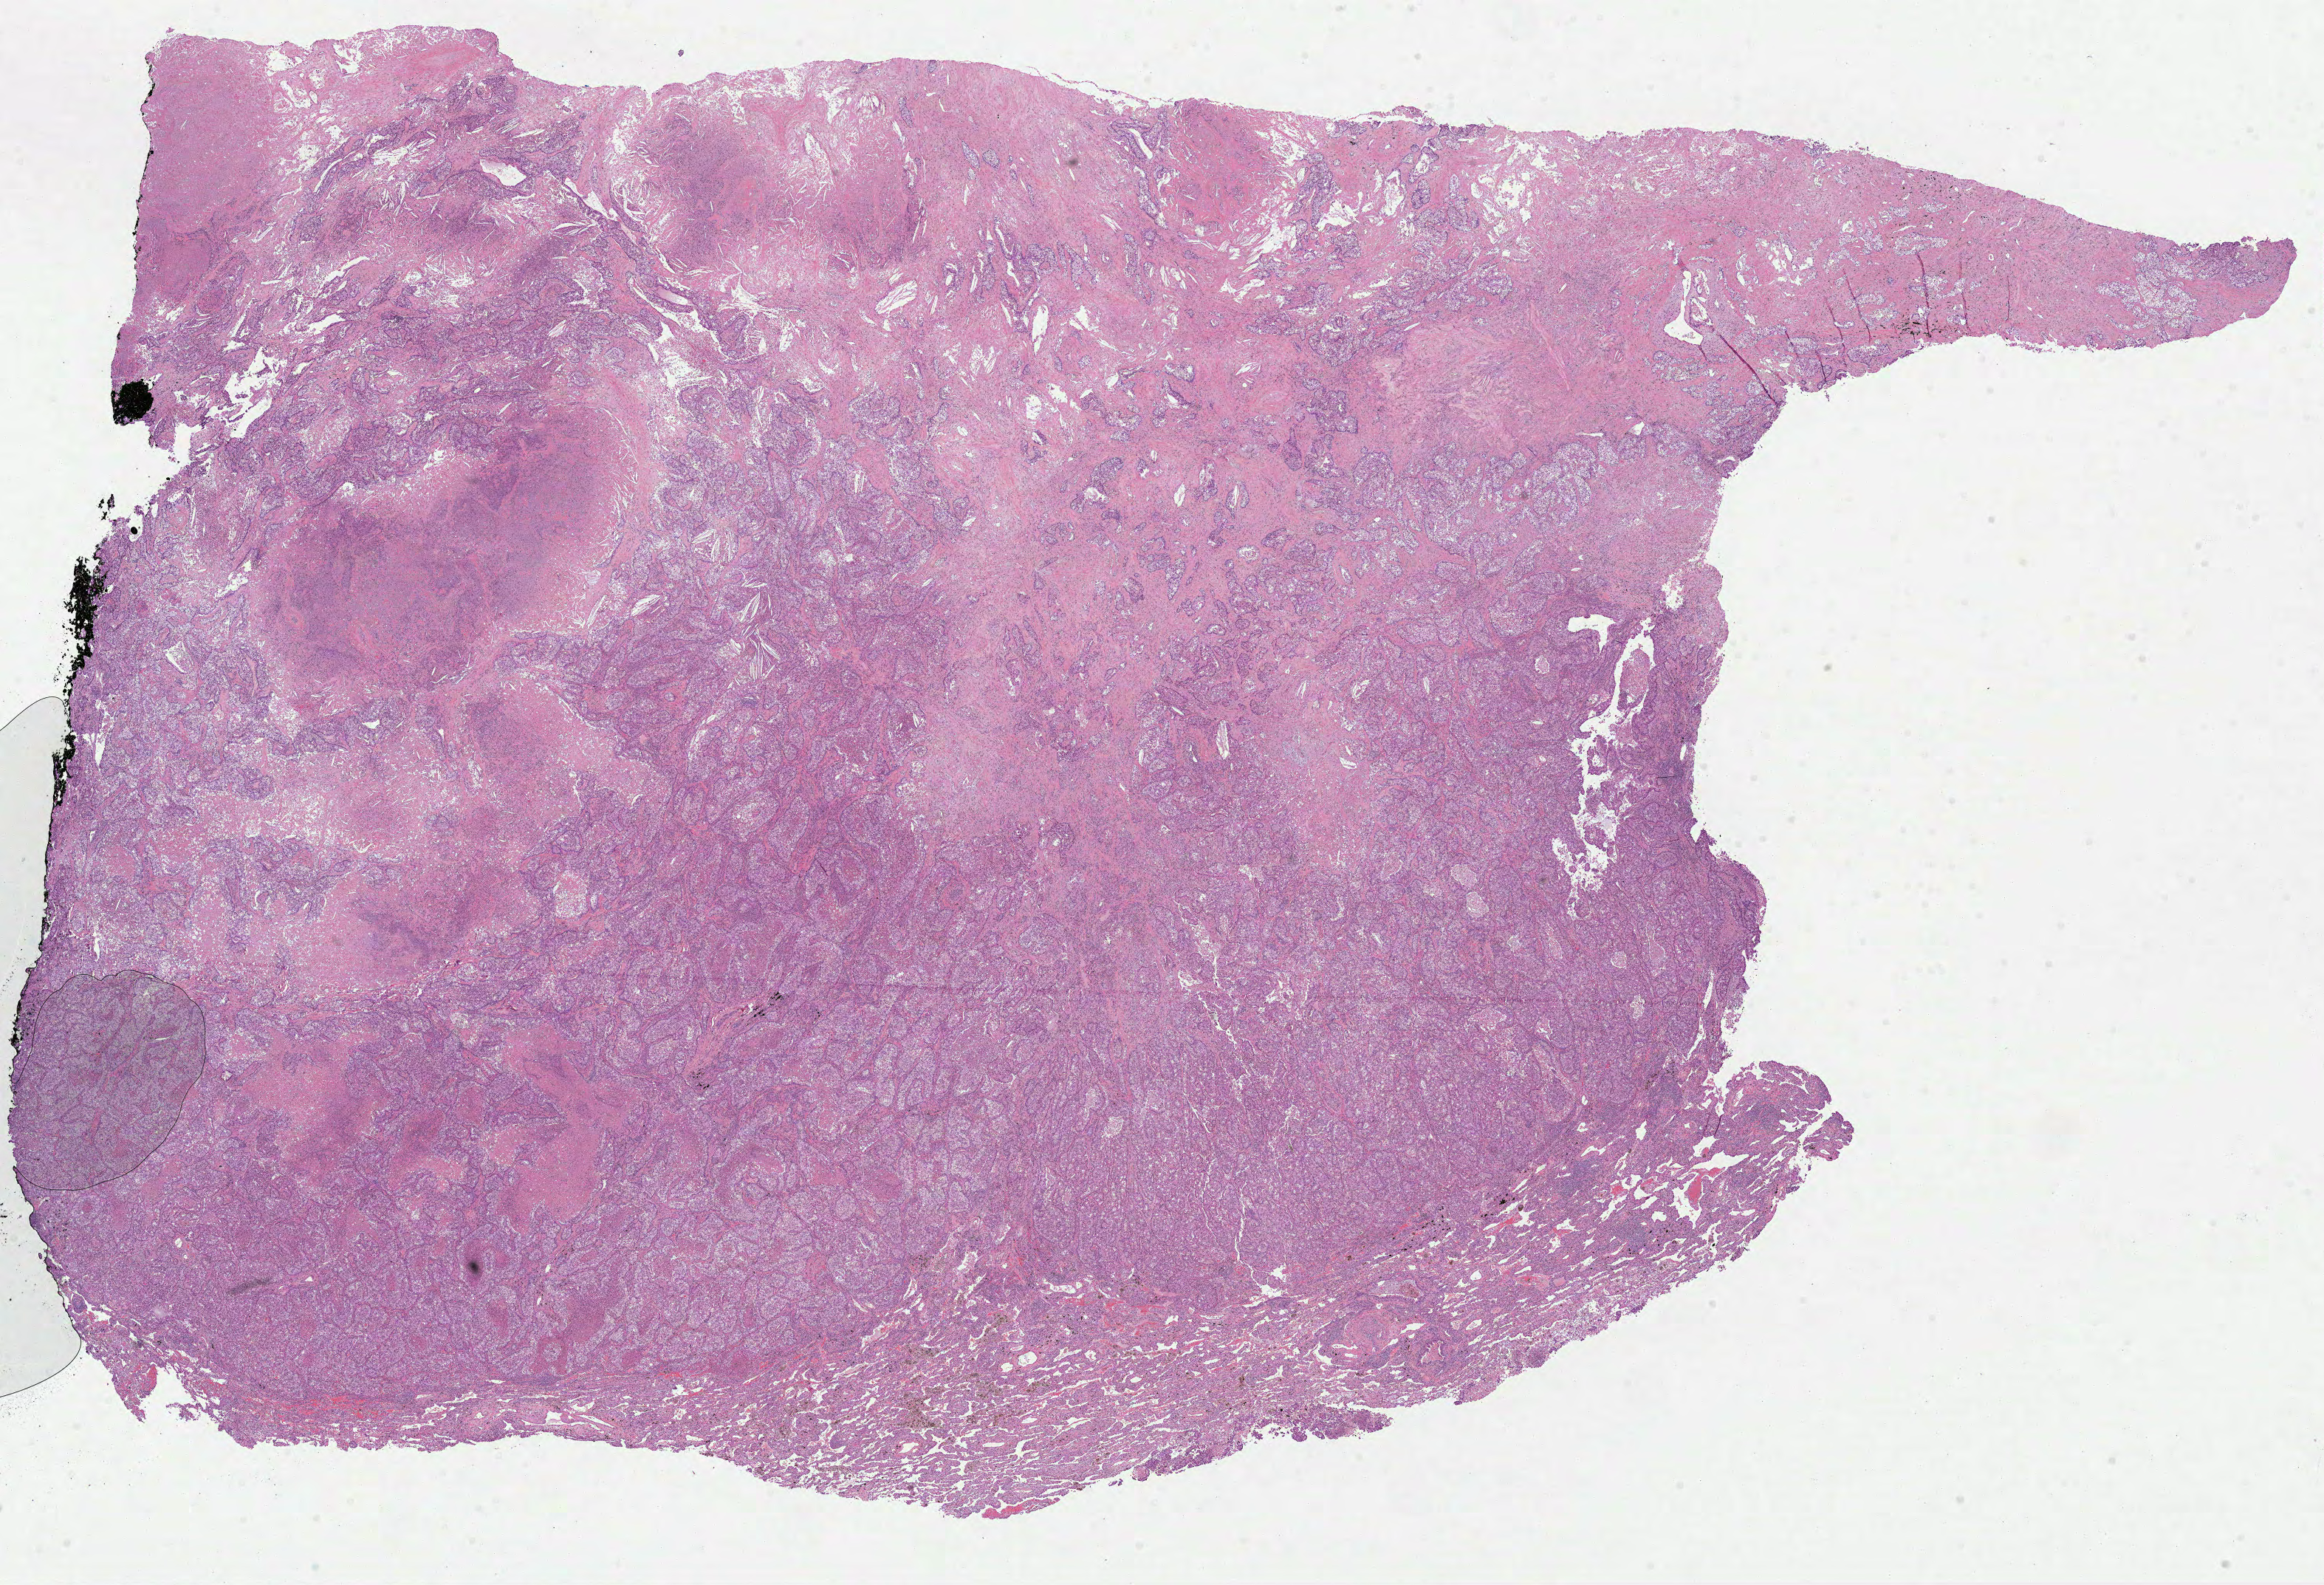
Whole-slide histology image, H&E-stained, low-resolution overview of the scanned area, about 25.4 x 17.3 mm; FFPE section; primary tumour sample from the lung. Female, age 50 years at initial diagnosis.
Diagnosis: Adenocarcinoma, NOS.